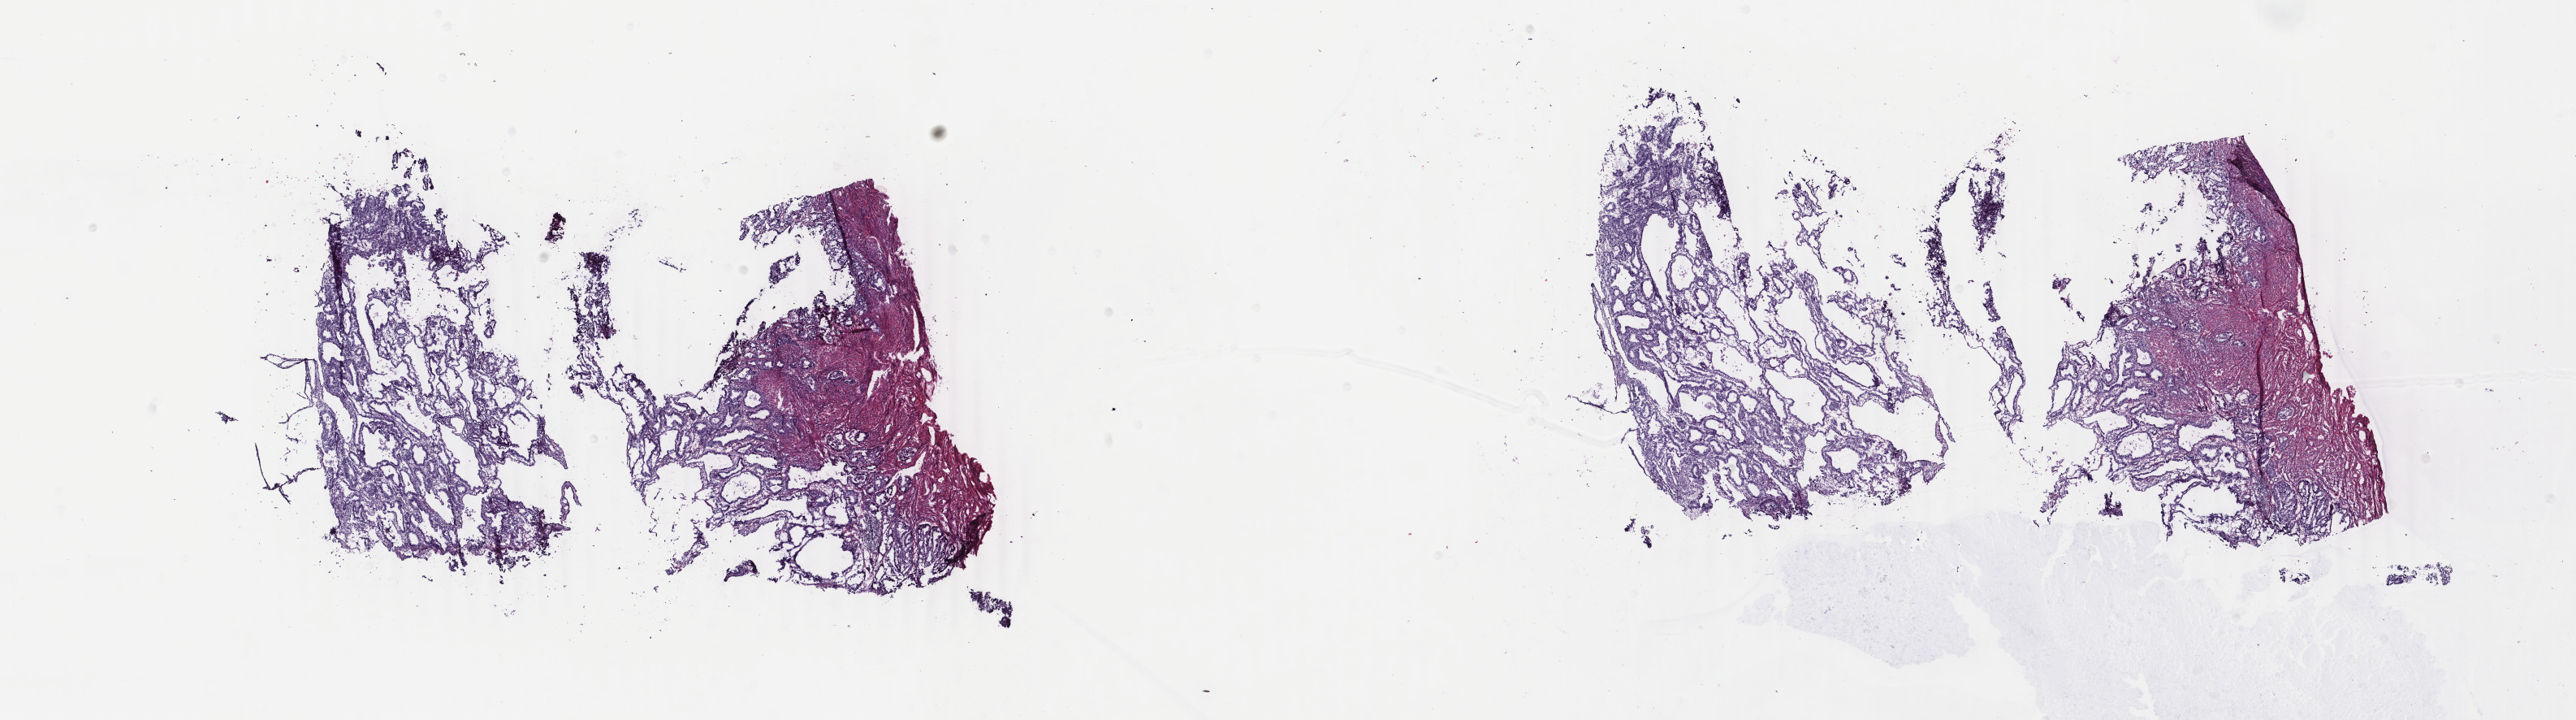
Whole-slide histology image, H&E, low-resolution overview of the scanned area, about 25.2 x 7.0 mm (acquisition: 40x scan); frozen section from the bottom of the tissue portion; uterus, primary tumour sample. Female patient; age at initial diagnosis 63 years. Histologic grade: G1 (well differentiated). Pathologist review of this section (percent, as recorded): tumour cells 80%, tumour nuclei 65%, normal cells 20%, stromal cells 0%, necrosis 0%. Infiltration values recorded for this section: lymphocyte infiltration 0%, monocyte infiltration 0%, neutrophil infiltration 0%.
Pathologic diagnosis: Endometrioid adenocarcinoma, NOS. FIGO stage: IIIA.